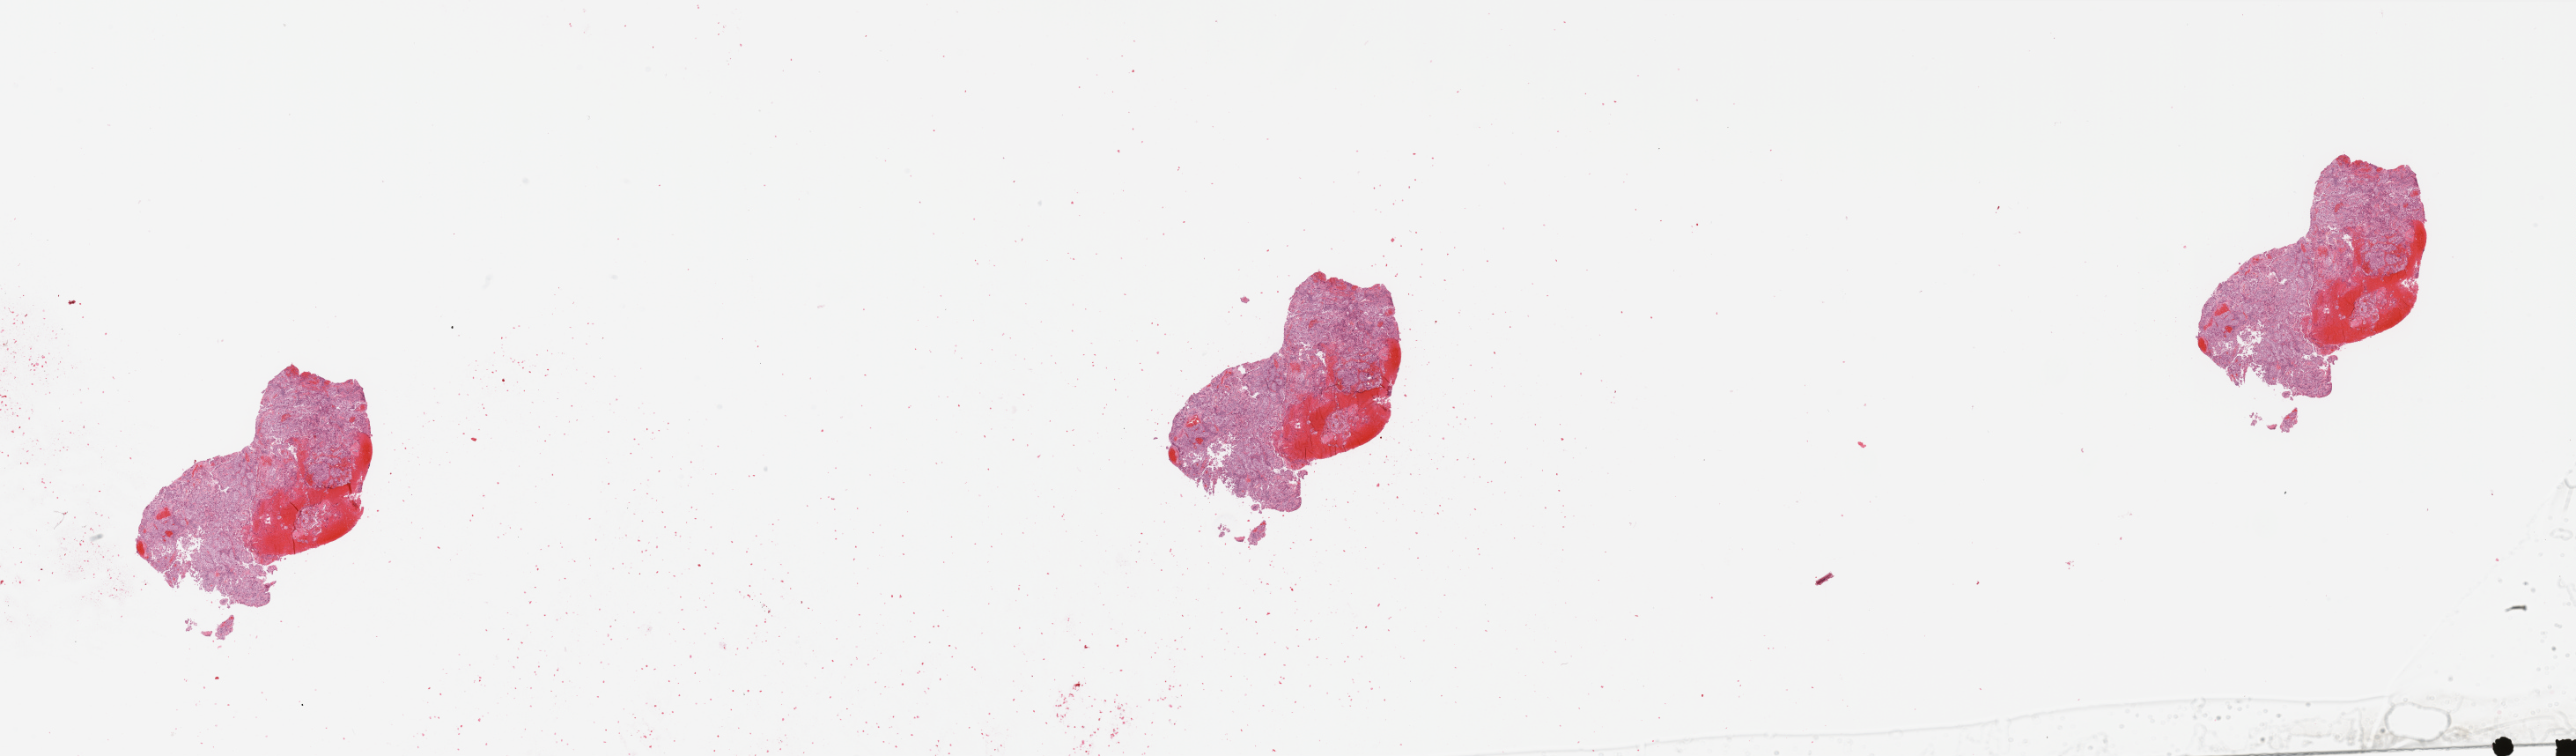
Digitized H&E-stained tissue section (whole slide), low-resolution overview of the scanned area, about 46.3 x 13.6 mm, tumour tissue sample, sampled site: uterus. Female, 85 y/o. Histologic grade: G3 (poorly differentiated). Composition of this section per pathologist review: tumour nuclei 95%, necrosis 5%.
• AJCC pathologic stage: II
• diagnosis: Endometrioid adenocarcinoma, NOS